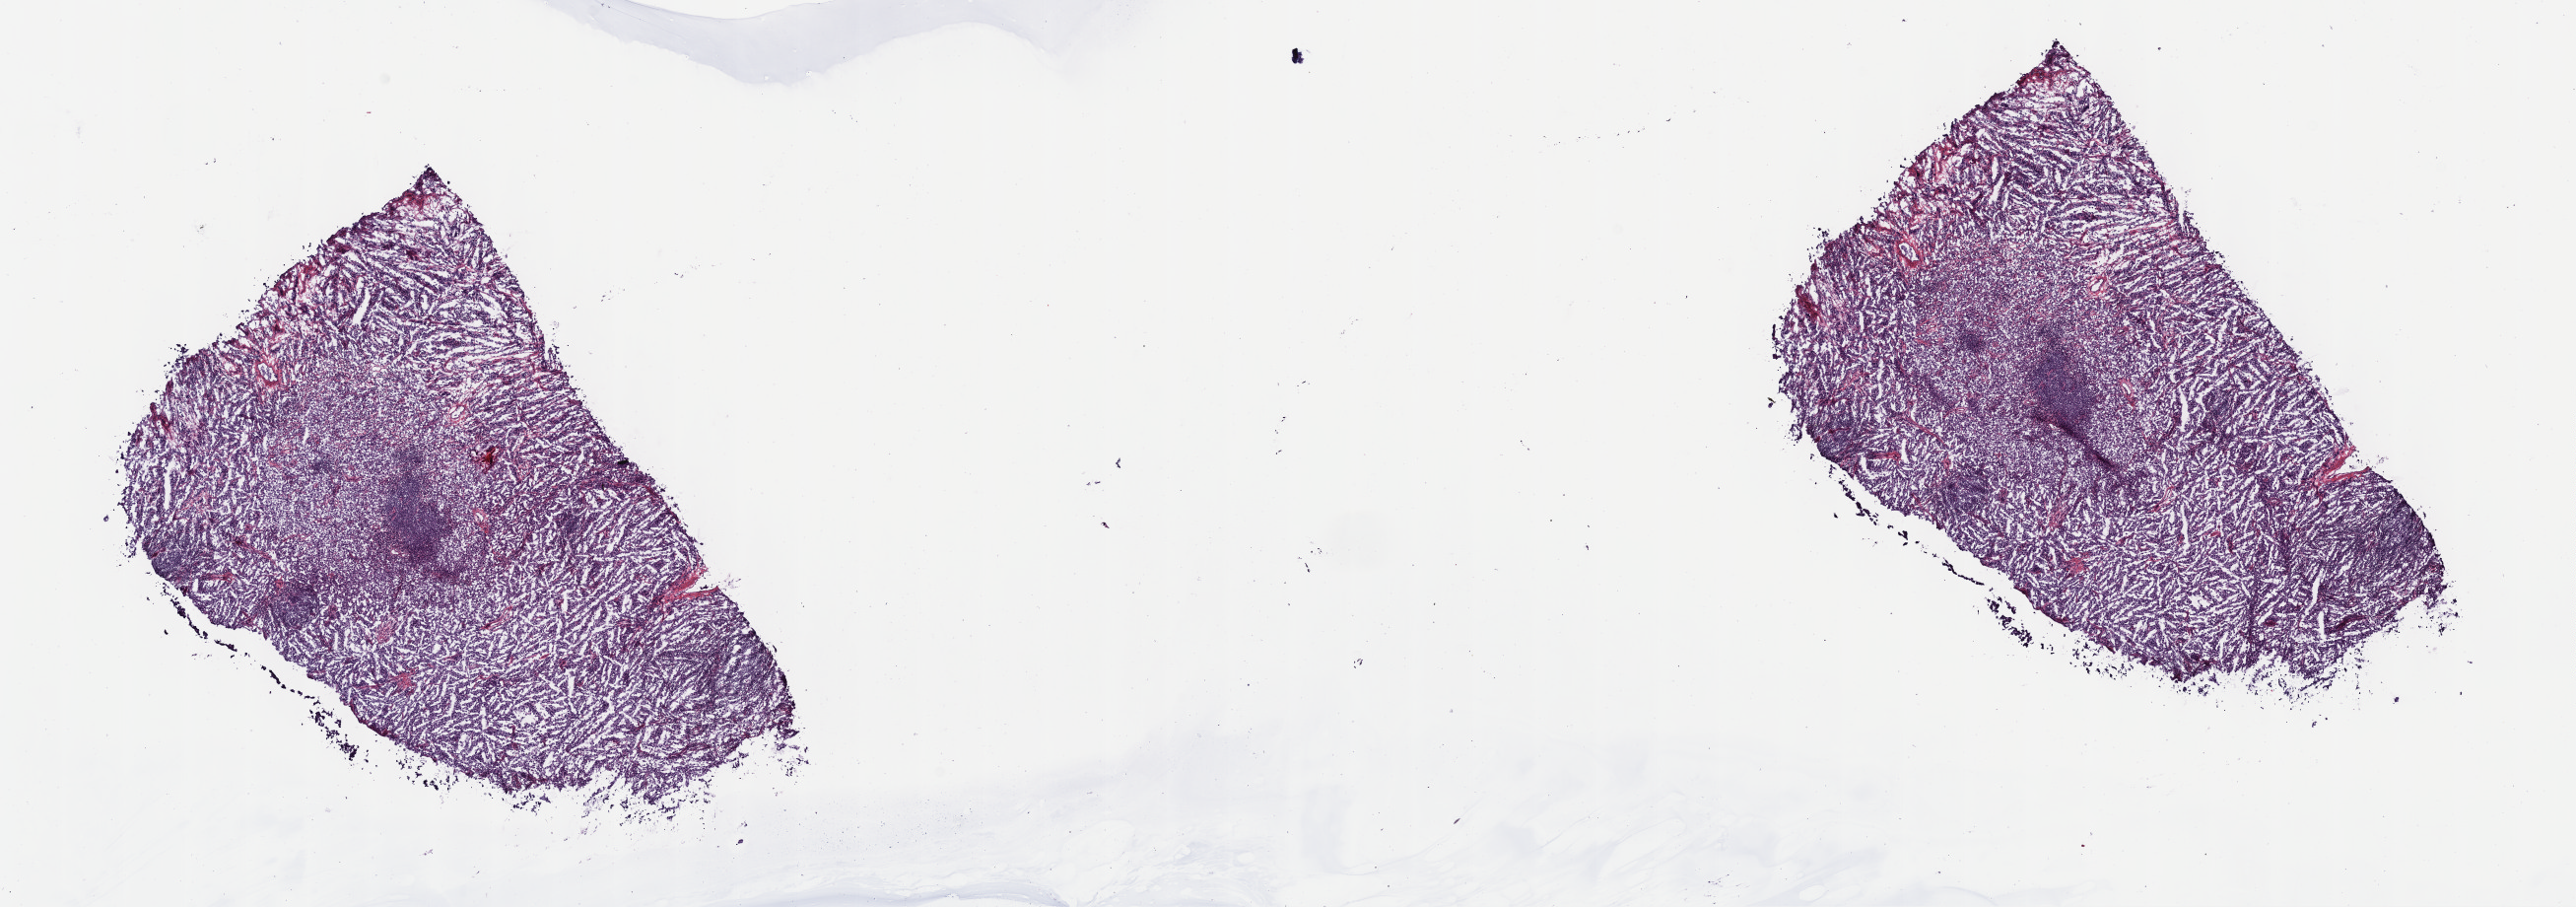
Digitized H&E tissue section (whole slide) — shown as a low-resolution overview of the whole scanned area (about 21.1 x 7.4 mm); frozen section from the top of the tissue portion; testis, additional new primary tumour sample. Patient: male, age at initial diagnosis 33 years. Composition of this section per pathologist review: tumour cells 85%, tumour nuclei 72%, normal cells 0%, stromal cells 14%, necrosis 1%. Inflammatory infiltration, as recorded: lymphocyte infiltration 25%, monocyte infiltration 0%, neutrophil infiltration 0%.
• this section: additional new primary tumour
• patient diagnosis: Mixed germ cell tumor